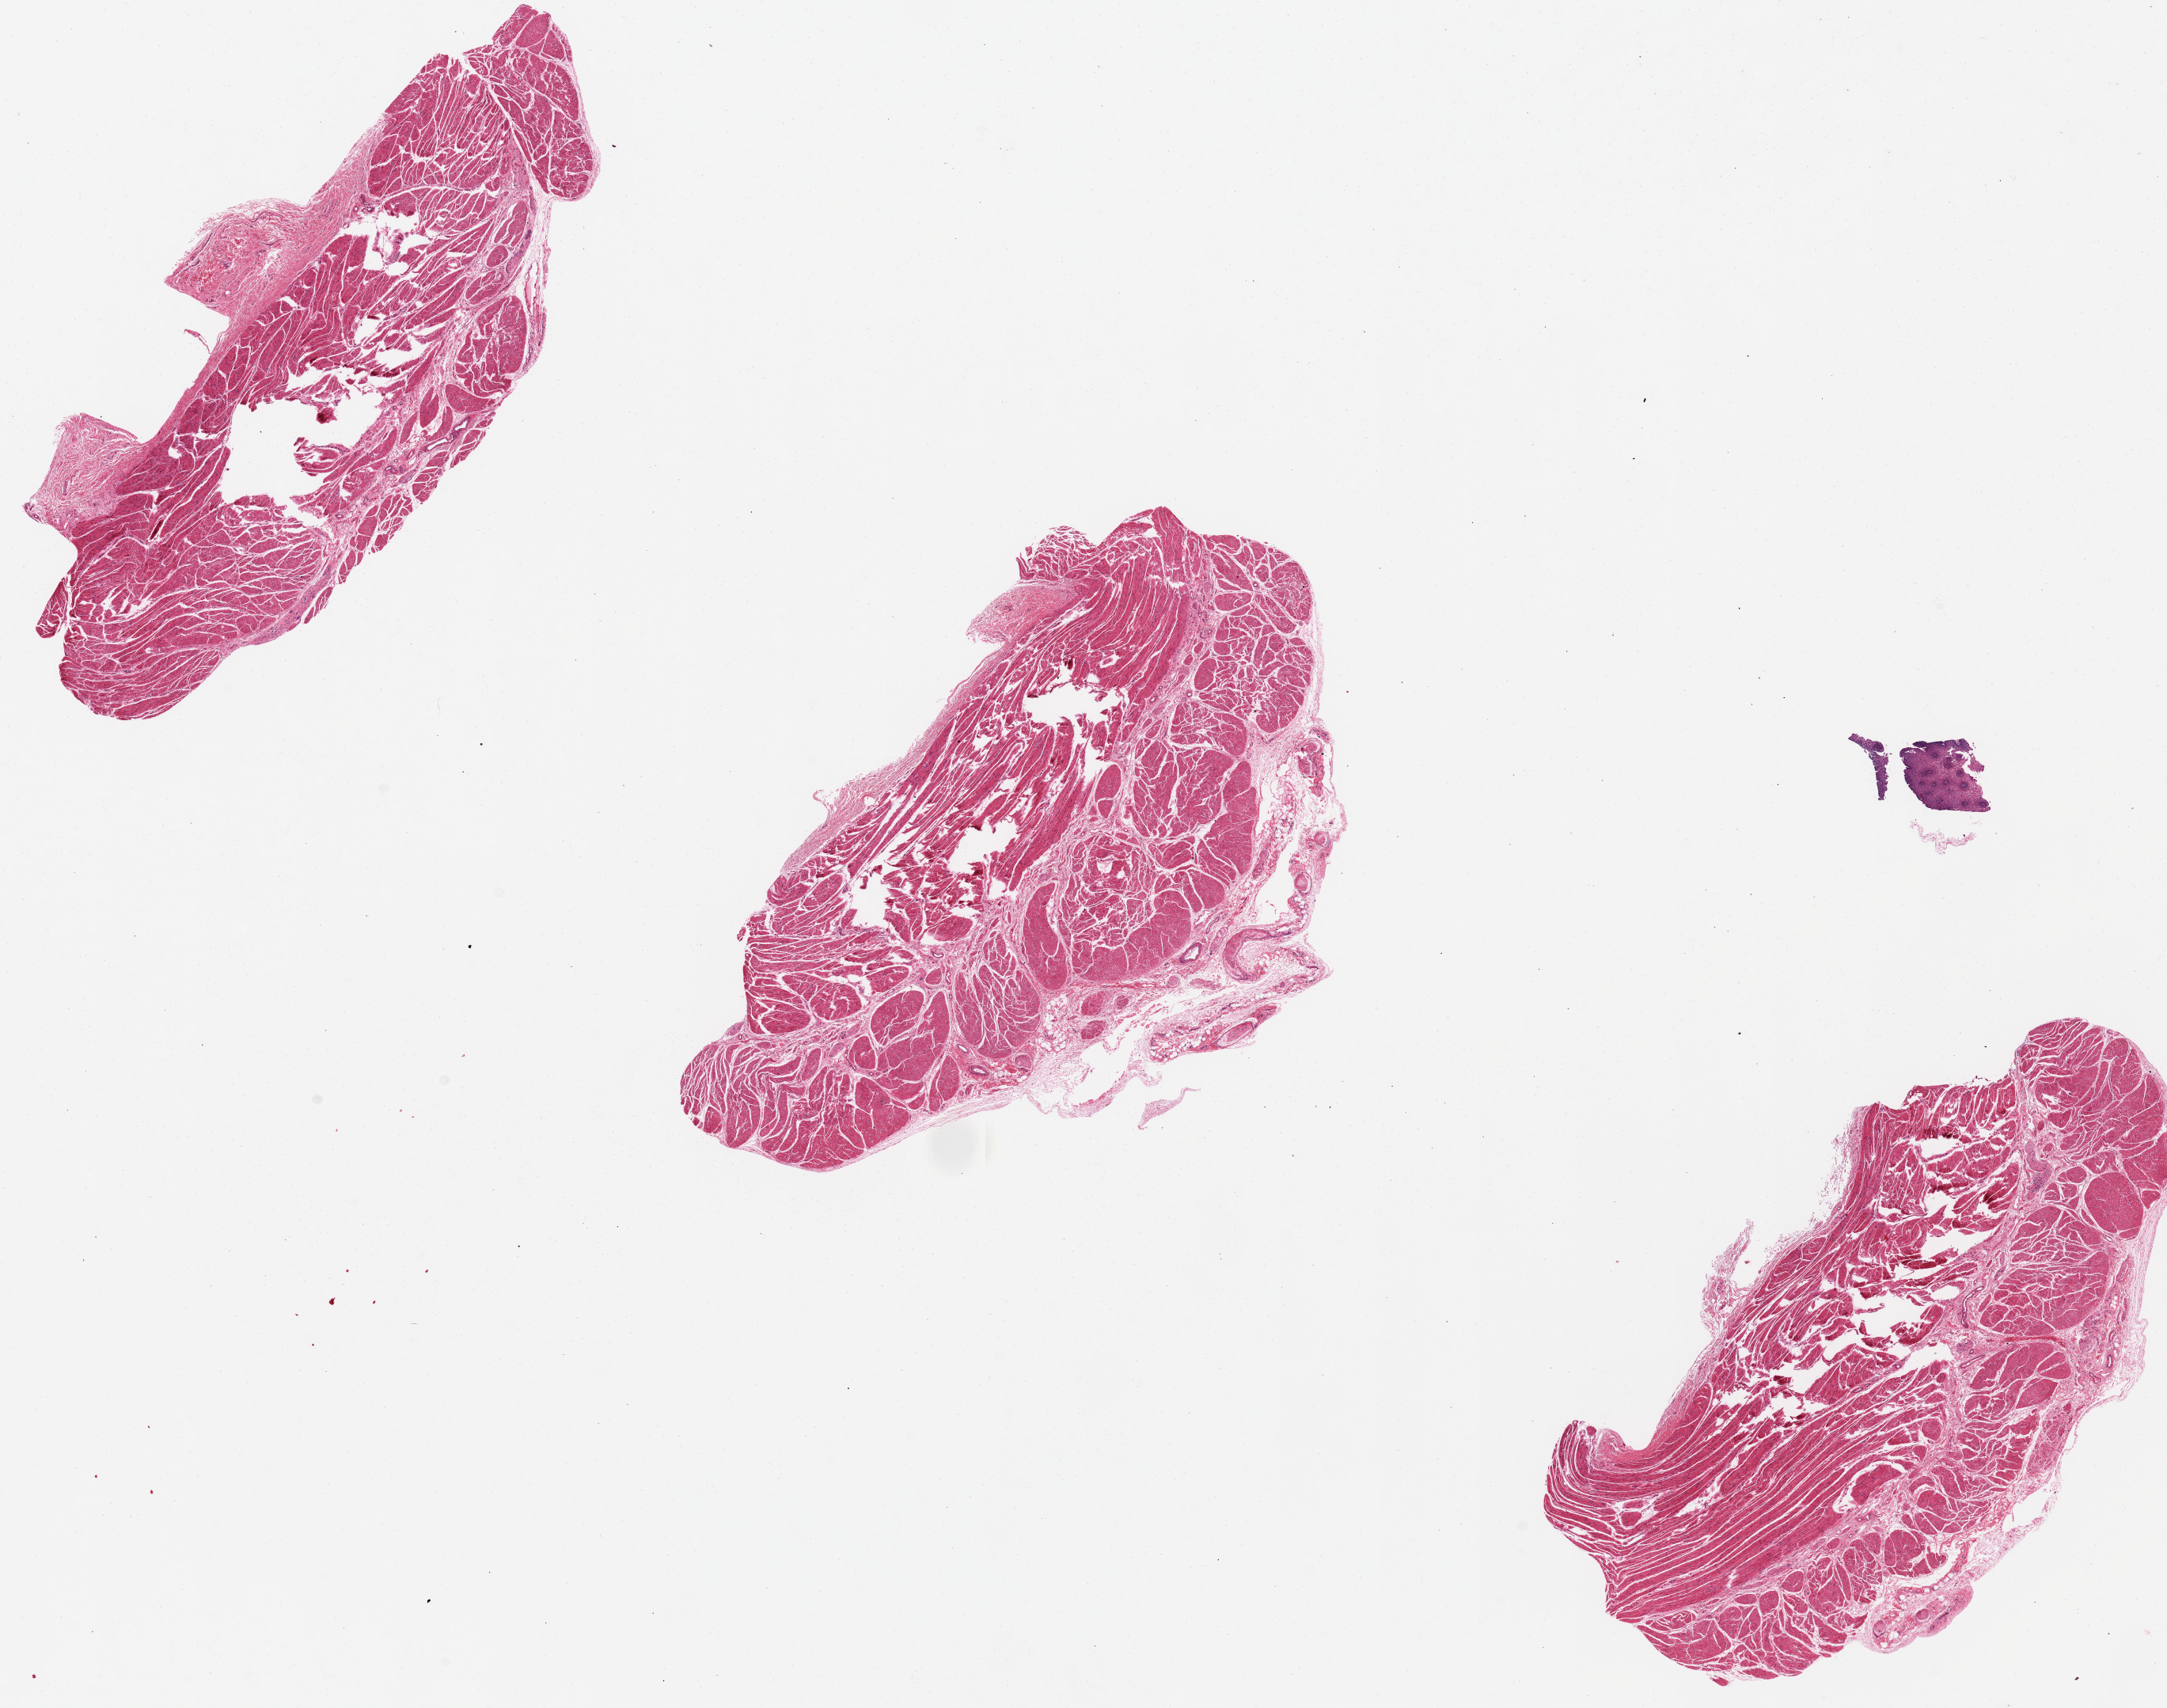
Haematoxylin and eosin whole-slide image, whole scanned area (about 21.7 x 17.1 mm) shown as a low-resolution overview. PAXgene-fixed paraffin-embedded (PFPE) section. Target tissue: esophageal muscle. Donor tissue sample. Male donor.
* pathologist's review note for this sample: 6 pieces